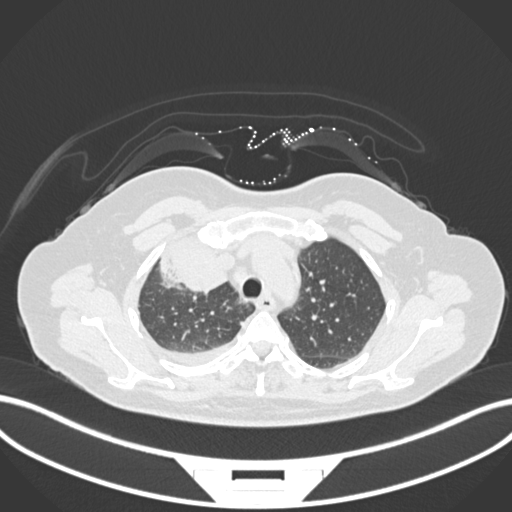
Chest CT, one axial slice; position 127 of 172 along the scan axis; lung window (W 1500 / L -600 HU); 1 mm slice thickness; 512 × 512 image matrix, field of view 400 × 400 mm. Female patient, age 52 years. From the clinical record (not read from this slice): clinical TNM (as recorded): T3 N1 M1.
Annotated regions visible in this slice (rectangle marked by the reading radiologist):
- lung tumour (recorded histology: adenocarcinoma): bounding box (x1, y1, x2, y2) in pixels: (155, 247, 230, 294)